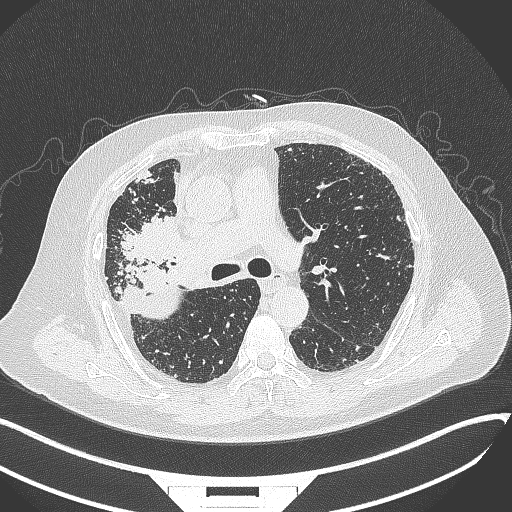
Chest CT, one axial slice; position 216 of 384 along the scan axis; reconstruction kernel B70f; 120 kVp; lung window (W 1500 / L -600 HU); 1 mm slice thickness; 512 × 512 image matrix, field of view 400 × 400 mm. Male patient, age 69 years. Case-level facts recorded for this patient, not image findings: clinical TNM (as recorded): T4 N3 M1.
Structures marked on this image (rectangle marked by the reading radiologist):
- lung tumour (recorded histology: adenocarcinoma): bounding box (x1, y1, x2, y2) in pixels: (120, 213, 186, 261)